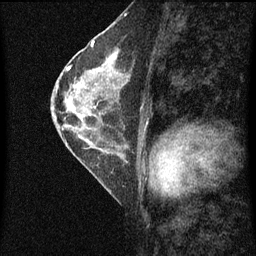
Breast MRI (dynamic contrast-enhanced), one sagittal slice; dynamic contrast-enhanced series, image 2 of 4 at this slice position (ordered by acquisition); 1.5 T; TE 4.2 ms, TR 8 ms; 256 × 256 image matrix, field of view 180 × 180 mm. Patient: female, 56 years.
Annotated regions visible in this slice (semi-automatically segmented with operator editing):
- analysis volume of interest (the breast-tissue region the enhancement analysis was run in; not a lesion): bounding box [x1, y1, x2, y2] px = [56, 52, 130, 115]
- tumour enhancement mask (voxels above the 70 % enhancement threshold inside the analysis volume of interest): [111, 54, 116, 61]